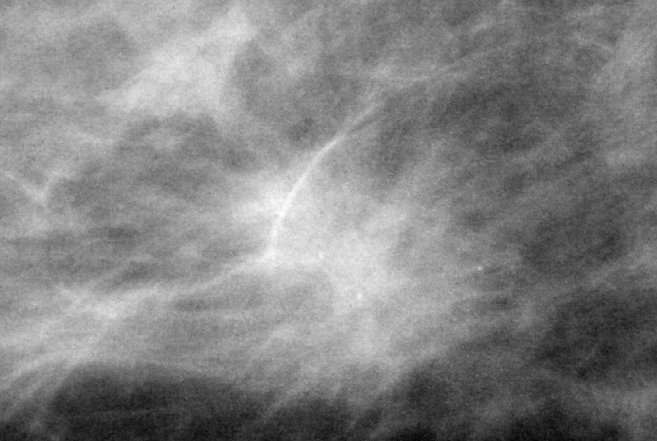
Cropped region of a digitized screen-film mammogram centred on a radiologist-marked abnormality; right breast; MLO view; BI-RADS breast density category 3 (scale 1–4).
Marked abnormality: calcifications, morphology punctate, distribution clustered; BI-RADS assessment category 5; subtlety rating 3 on a 1 (subtle) to 5 (obvious) scale; pathology result (as recorded, not read from the image): malignant.